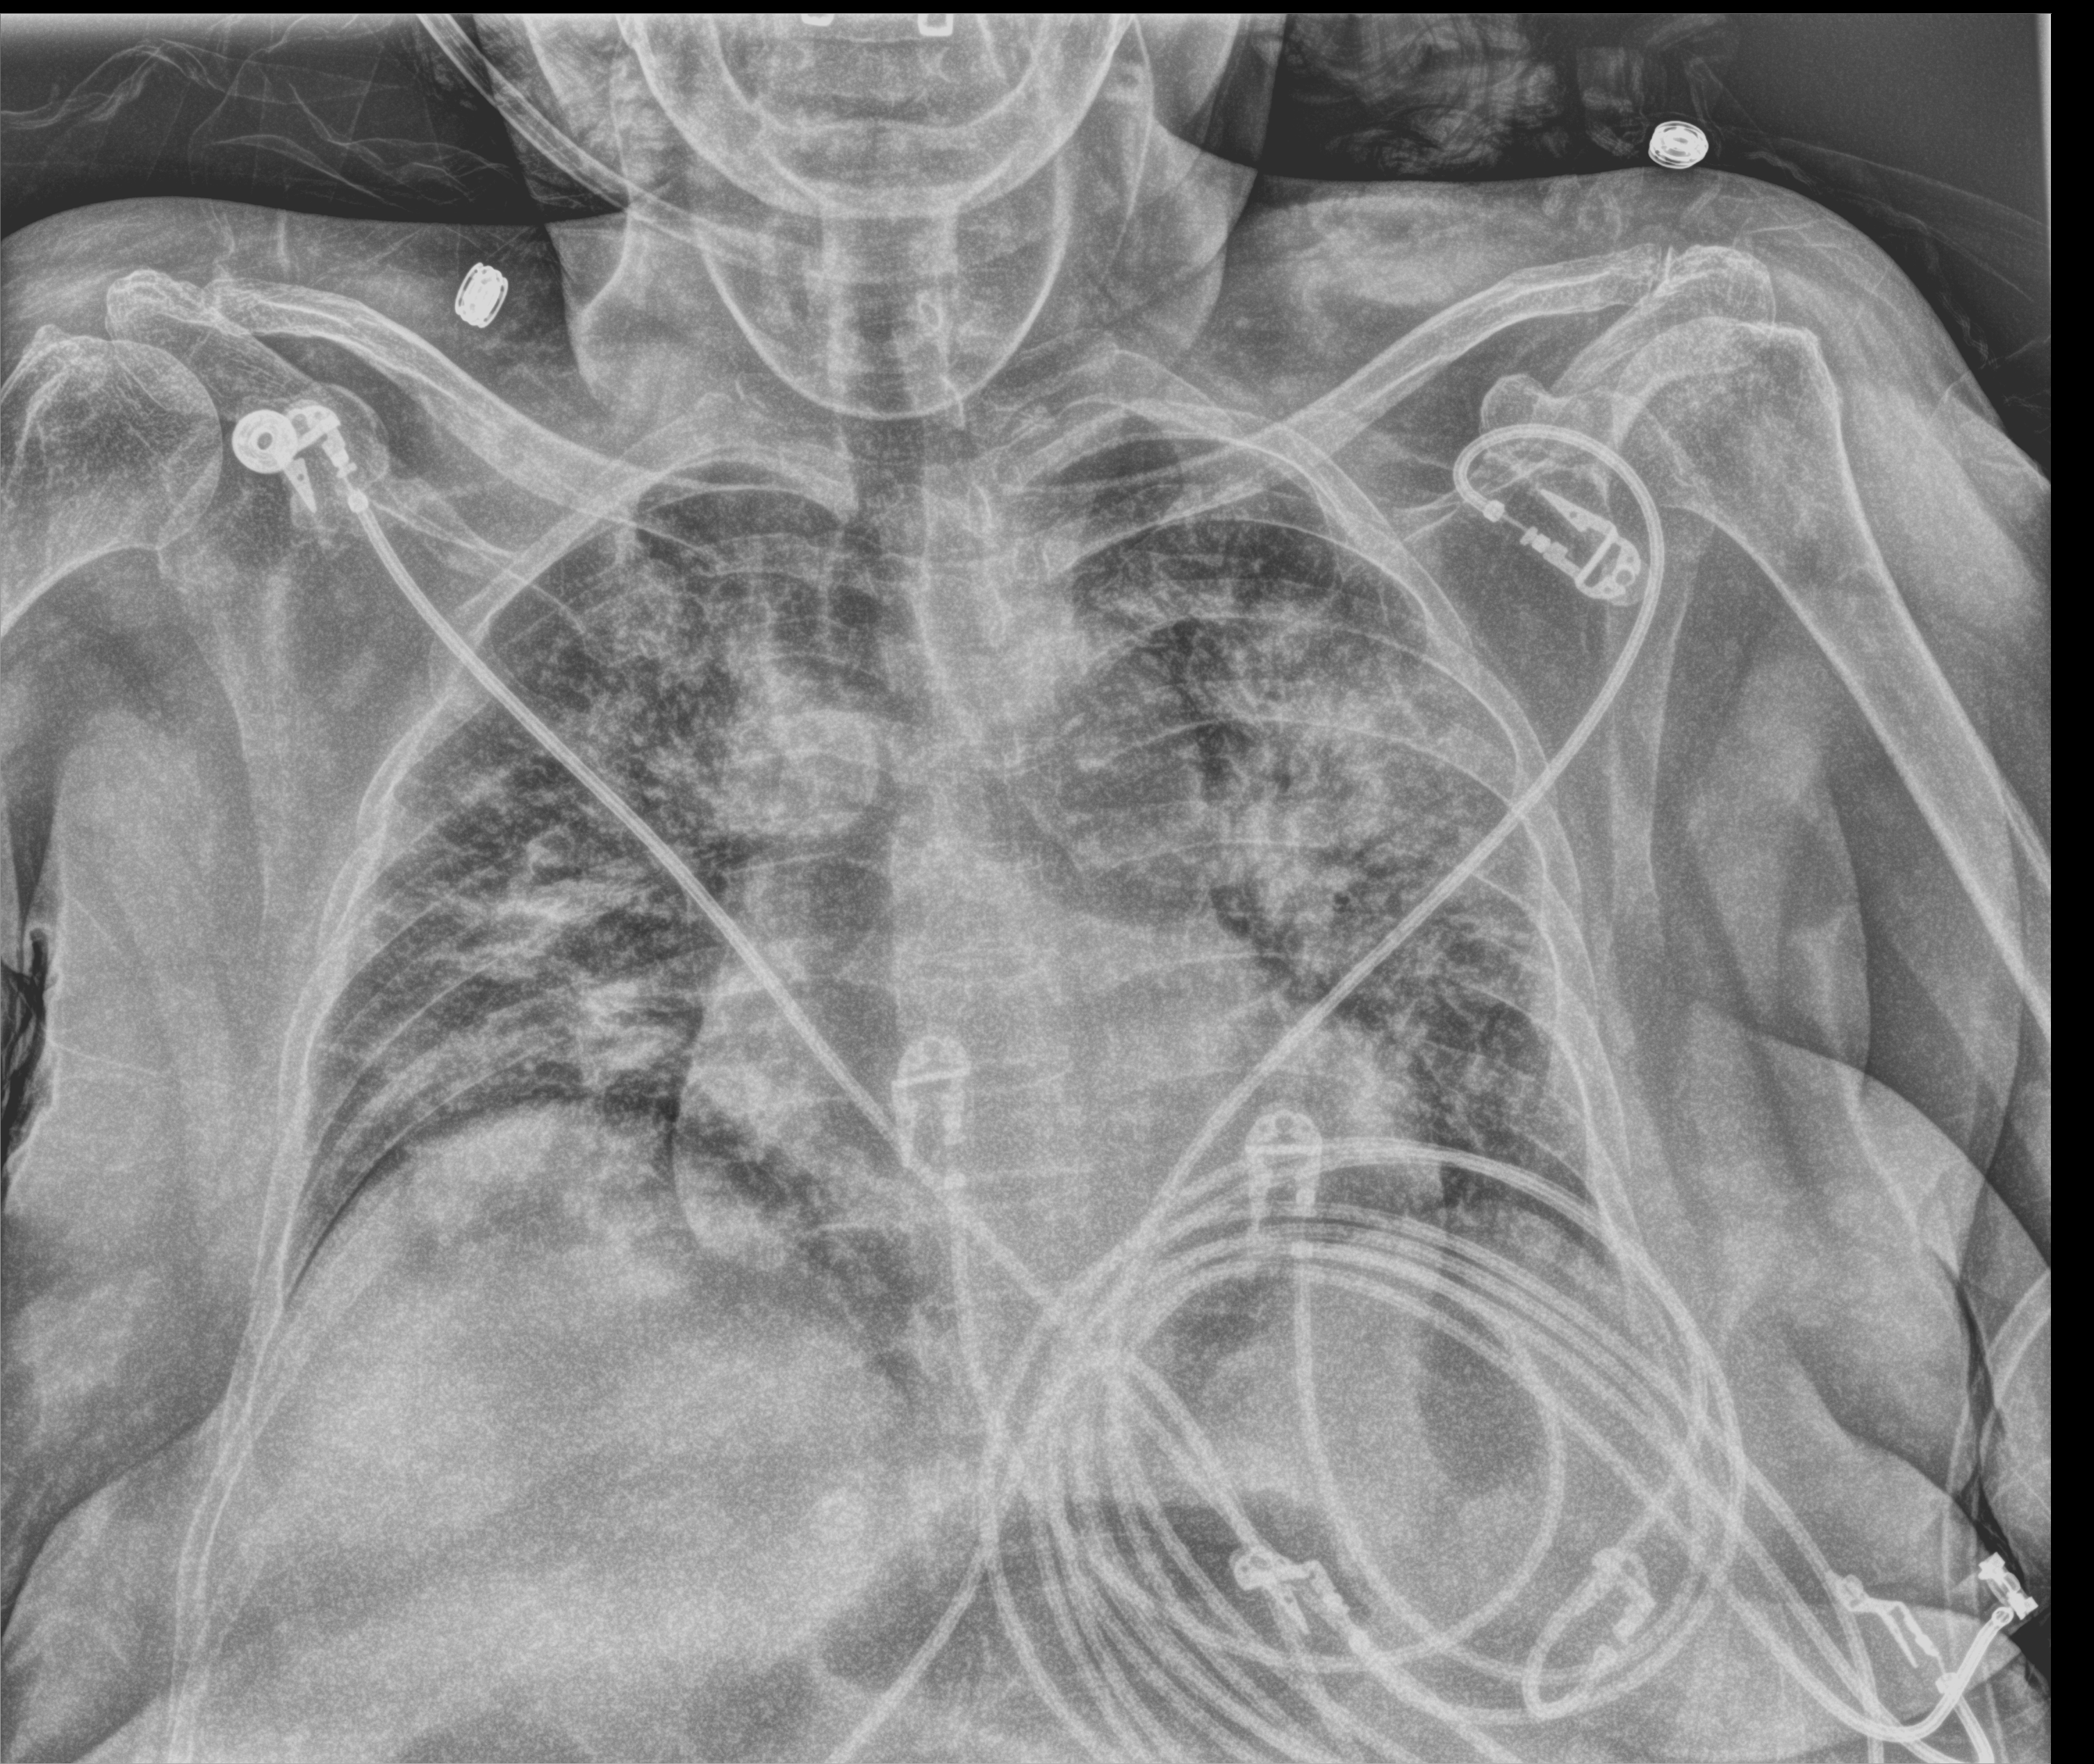
Chest X-ray (portable); anteroposterior (AP) projection. Female patient hospitalised with COVID-19, age 60–74 years.
Hospital-stay facts (about this admission, not read from this image; timing relative to this image not recorded):
- mechanically ventilated during this hospital stay: no
- COPD (admission record): no
- length of hospital stay: 11 days